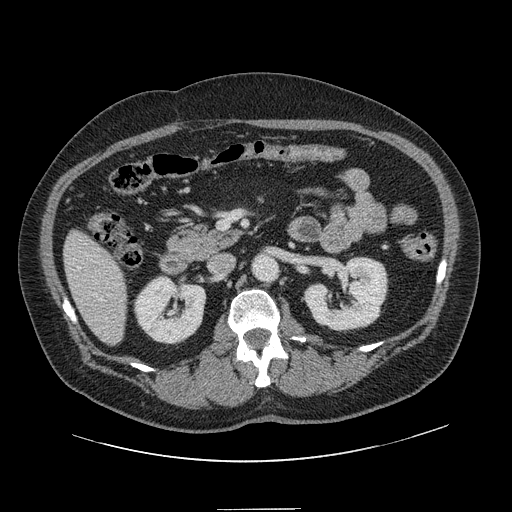
Contrast-enhanced abdominal CT, one axial slice. Slice 52 of 154 in the series (ordered by position). 120 kVp. Intravenous contrast given. Soft-tissue window (W 400 / L 40 HU). 512 × 512 image matrix. Male patient, age 61 years. Case-level facts recorded for this patient, not image findings: diagnosis: colorectal cancer liver metastases, imaged before liver resection; multiple liver metastases: yes; largest metastasis: 2.6 cm; disease in both lobes: yes.
Annotated regions visible in this slice (manually delineated by an expert):
- hepatic veins: bounding box <78,267,103,301> (left, top, right, bottom; pixels)
- liver: <65,232,126,344>
- planned liver remnant (the part of the liver to remain after resection): <65,231,126,344>